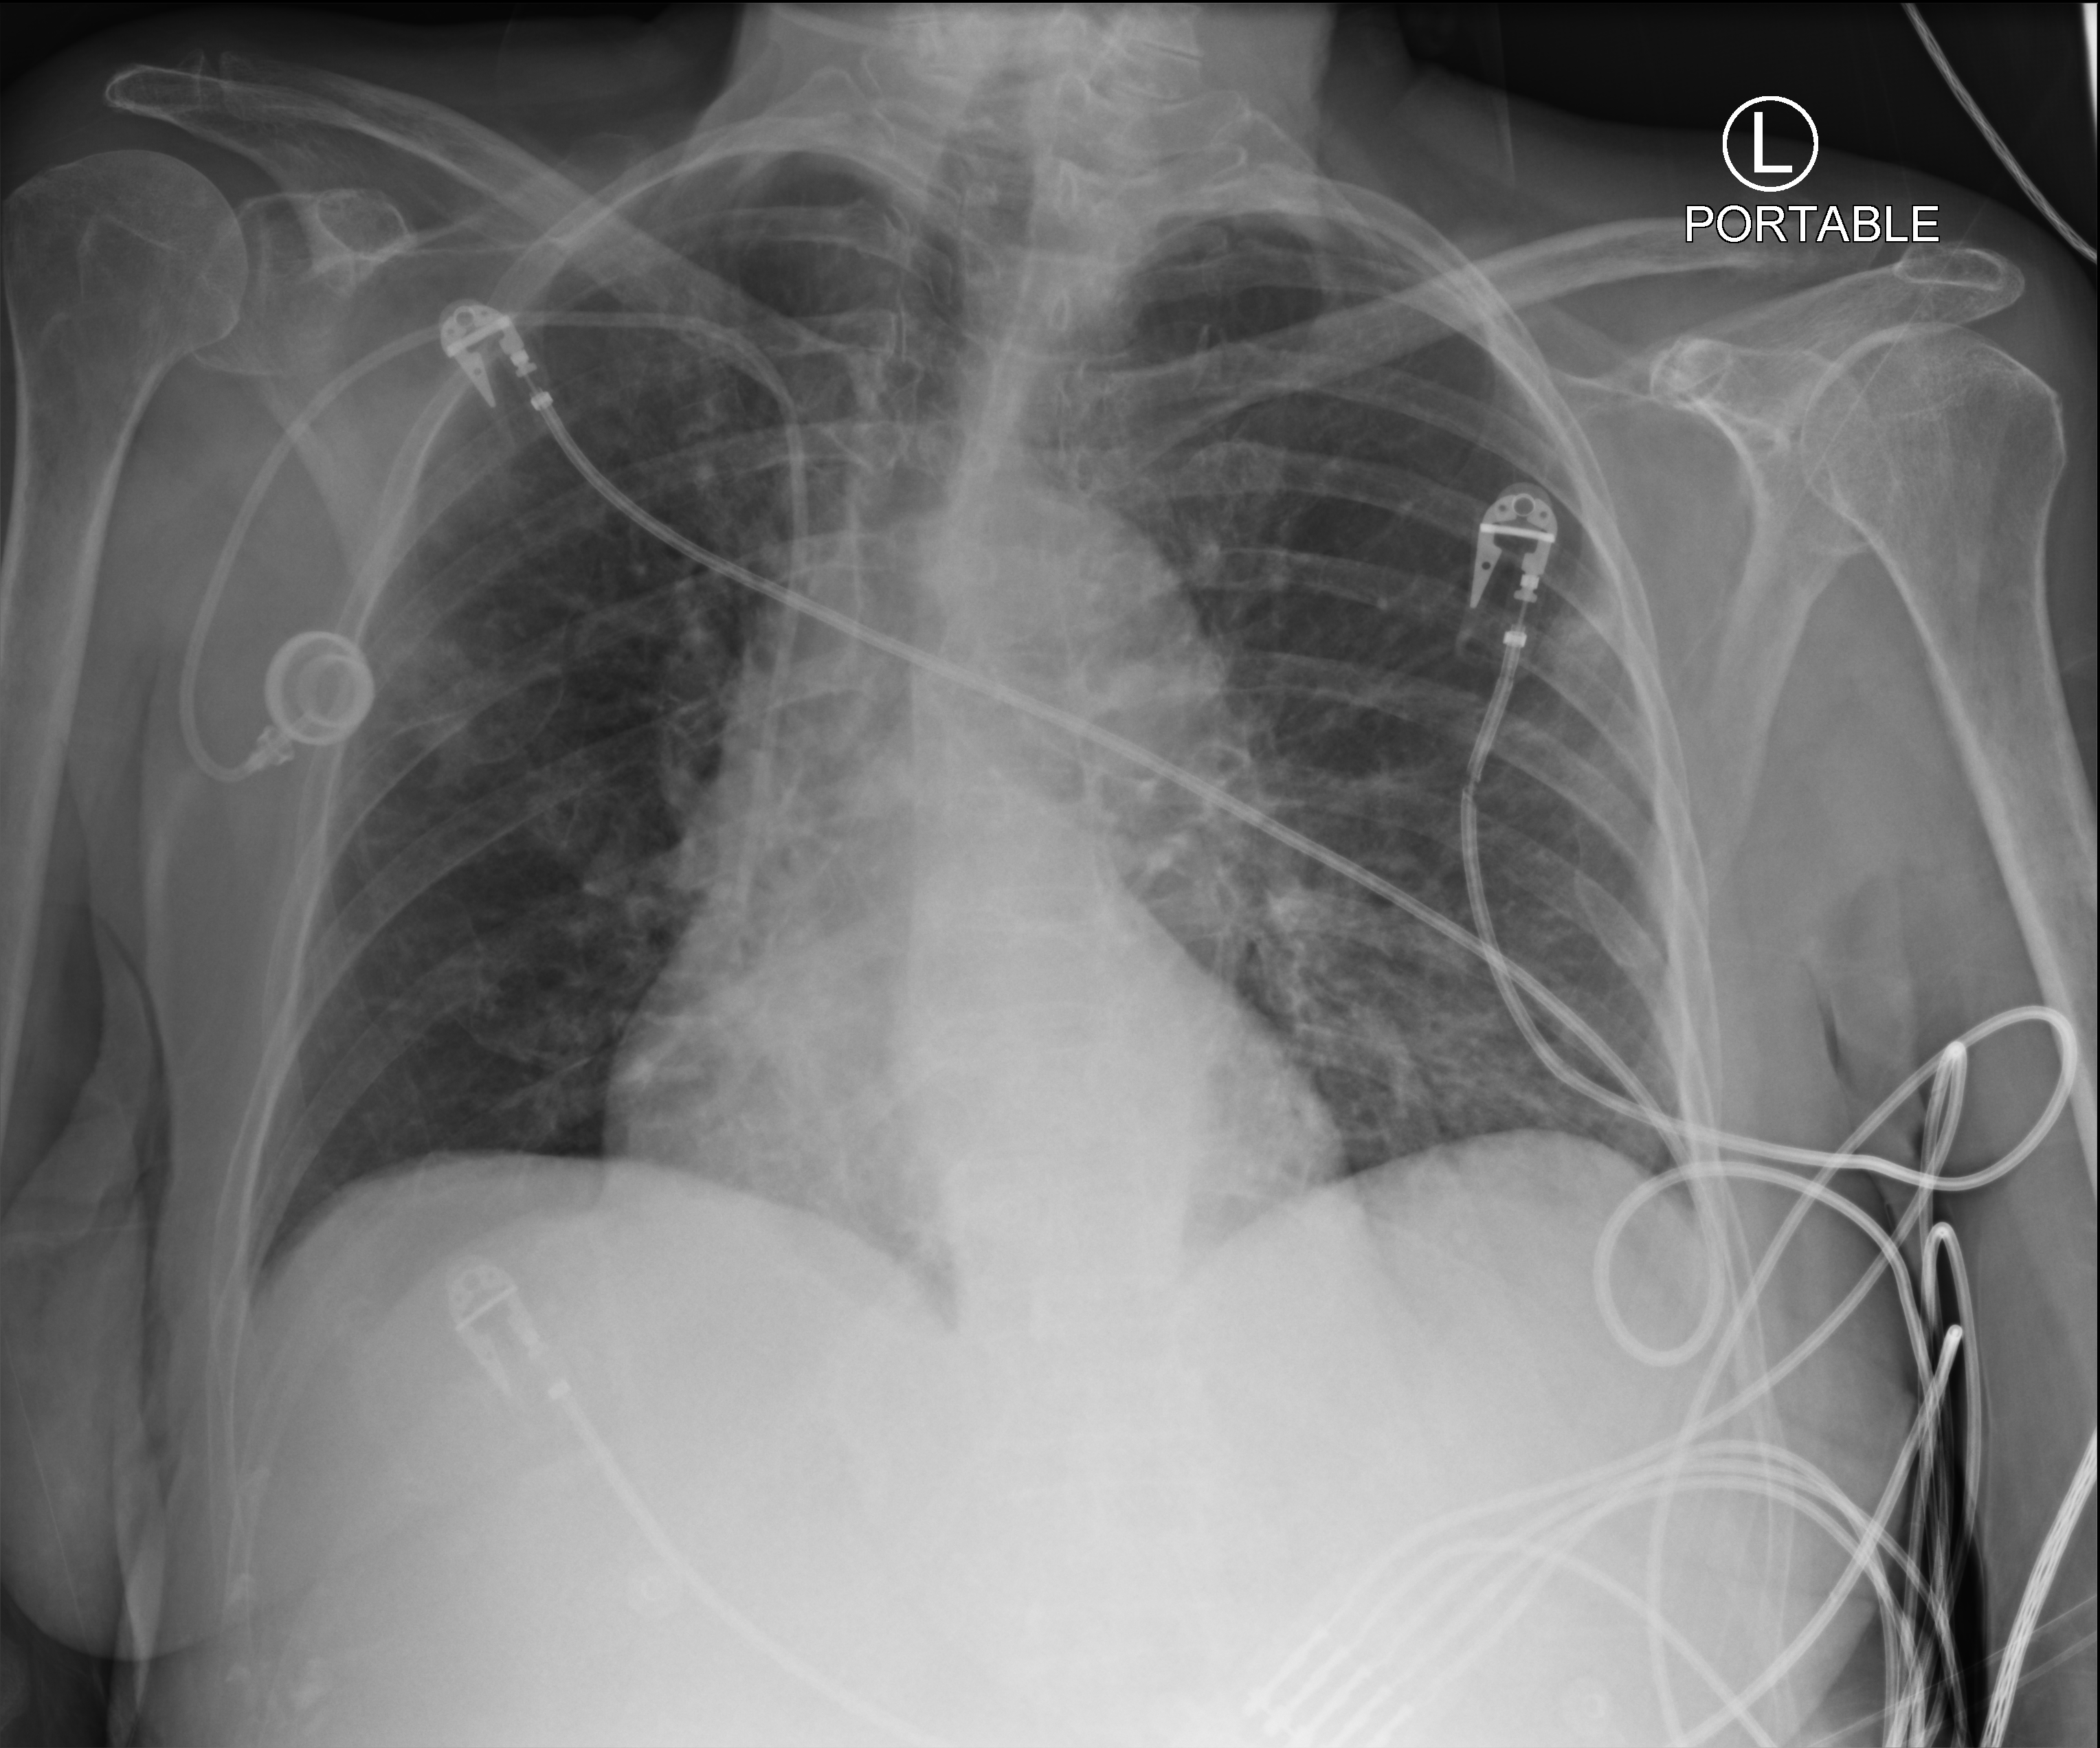
Chest X-ray (portable), anteroposterior (AP) projection. Female patient hospitalised with COVID-19, age 75–90 years.
Admission-level facts for this patient (not findings on this image; timing relative to this image not recorded):
- length of hospital stay: 7 days